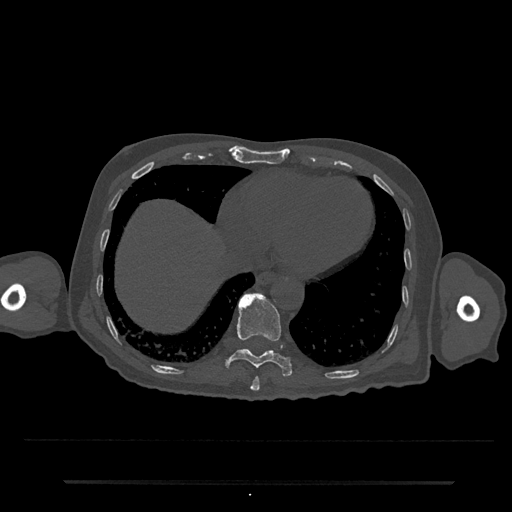
CT including the spine, one axial slice; slice 312 of 797 in the series (ordered by position); reconstruction kernel Br40s/3; 120 kVp; bone window (W 1800 / L 400 HU); 0.5 mm slice thickness; 512 × 512 image matrix, field of view 427 × 427 mm. Patient: male, 74 years. From the clinical record (not read from this slice): primary cancer: prostate.
Structures marked on this image (semi-automatic segmentation, software-assisted and operator-edited):
- T10 vertebra: box from (x=225, y=293) to (x=293, y=377) px
- T9 vertebra: (x=250, y=377)–(x=260, y=391)